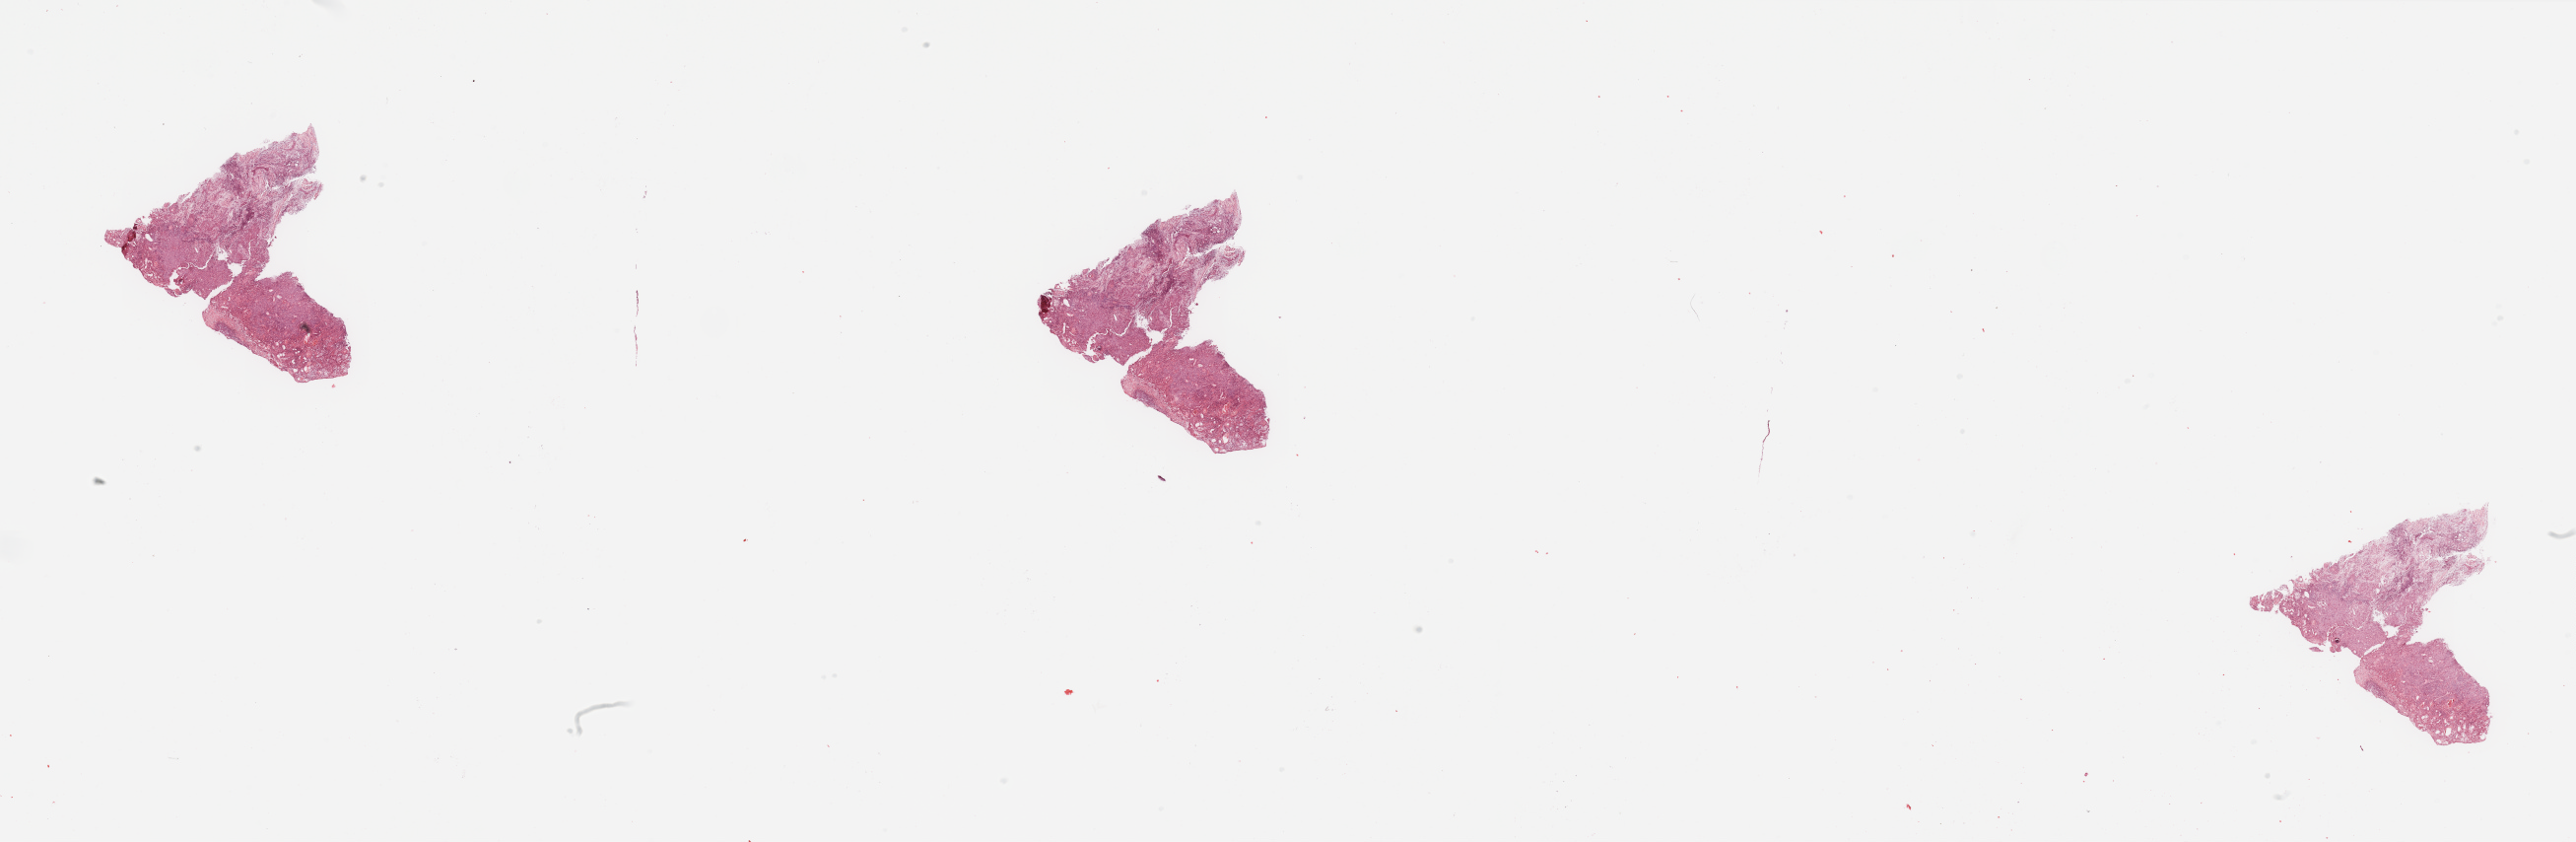
H&E-stained whole-slide image, shown as a low-resolution overview of the whole scanned area (about 41.3 x 13.5 mm). Tumour tissue sample, sampled site: tongue. Male, 57 y/o. Histologic grade: G2 (moderately differentiated). Pathologist review of this section (percent, as recorded): tumour nuclei 80%, necrosis 5%.
Primary tumour site (as recorded): oral cavity. AJCC pathologic stage: IVA. Histologic diagnosis: Squamous cell carcinoma, NOS (tongue, NOS).